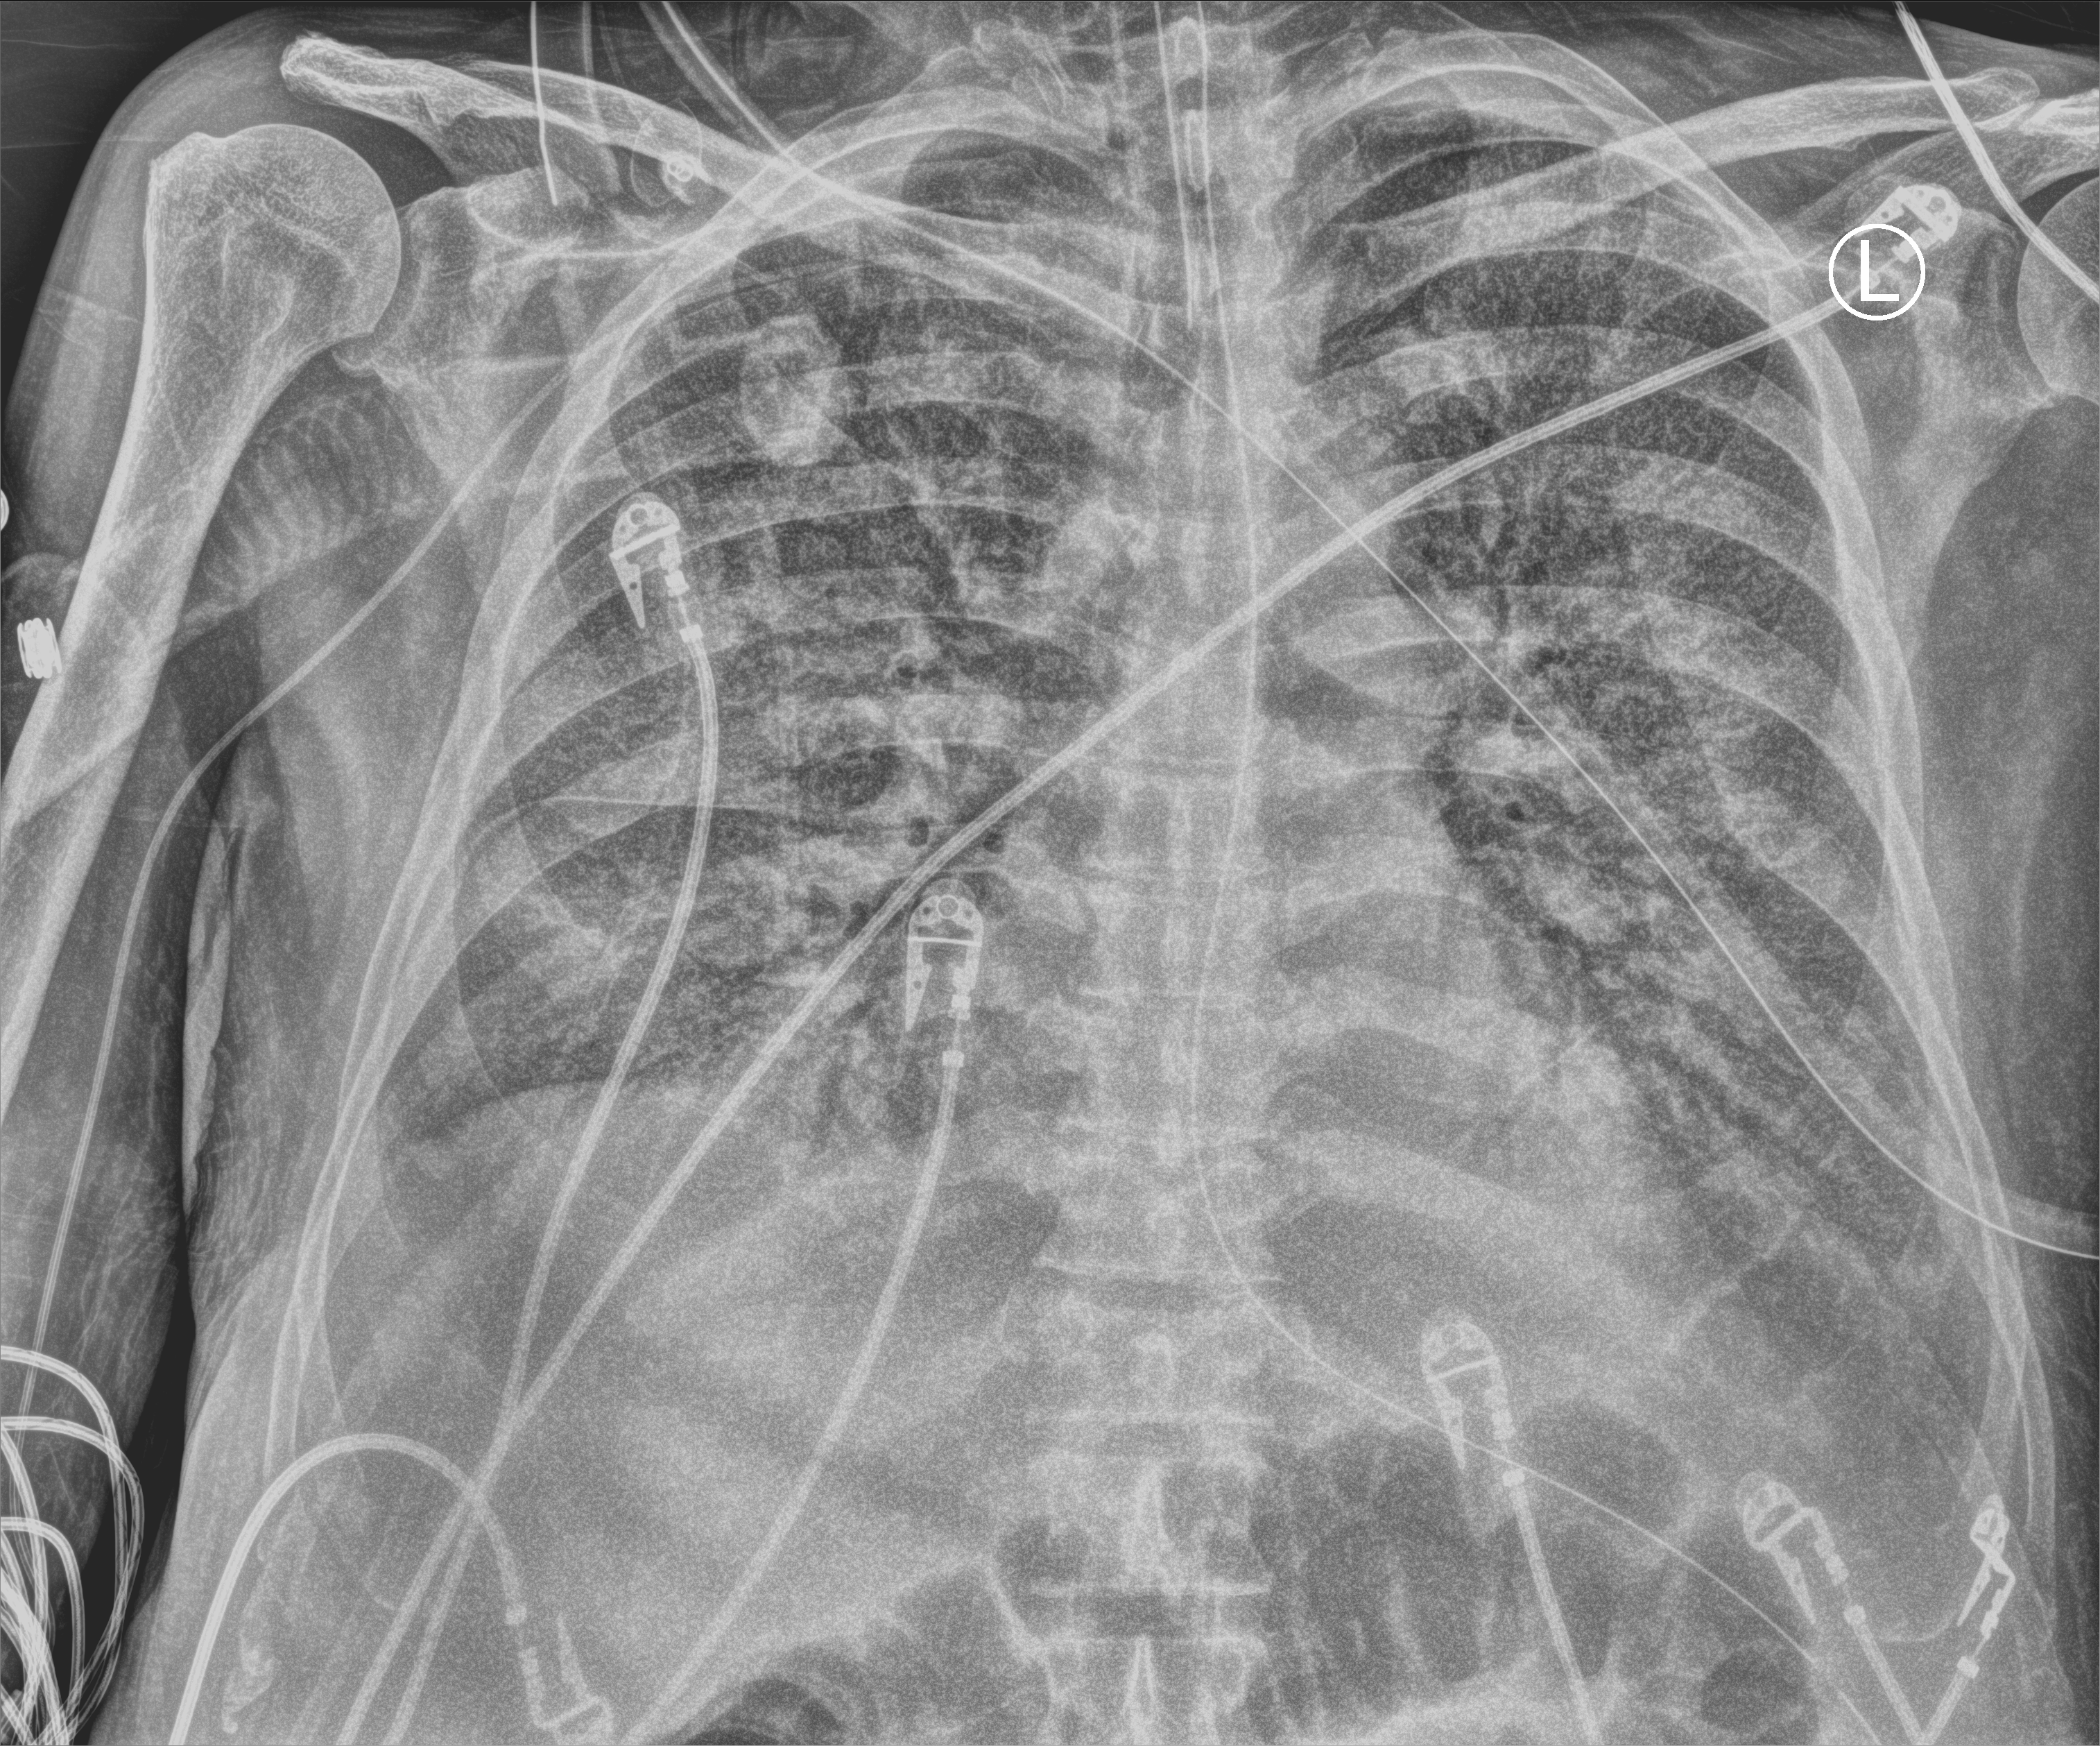
Chest X-ray (portable); anteroposterior (AP) projection. Male patient hospitalised with COVID-19, age 60–74 years.
Admission-level facts for this patient (not findings on this image; timing relative to this image not recorded): mechanically ventilated during this hospital stay: yes; admitted to intensive care during this hospital stay: yes.